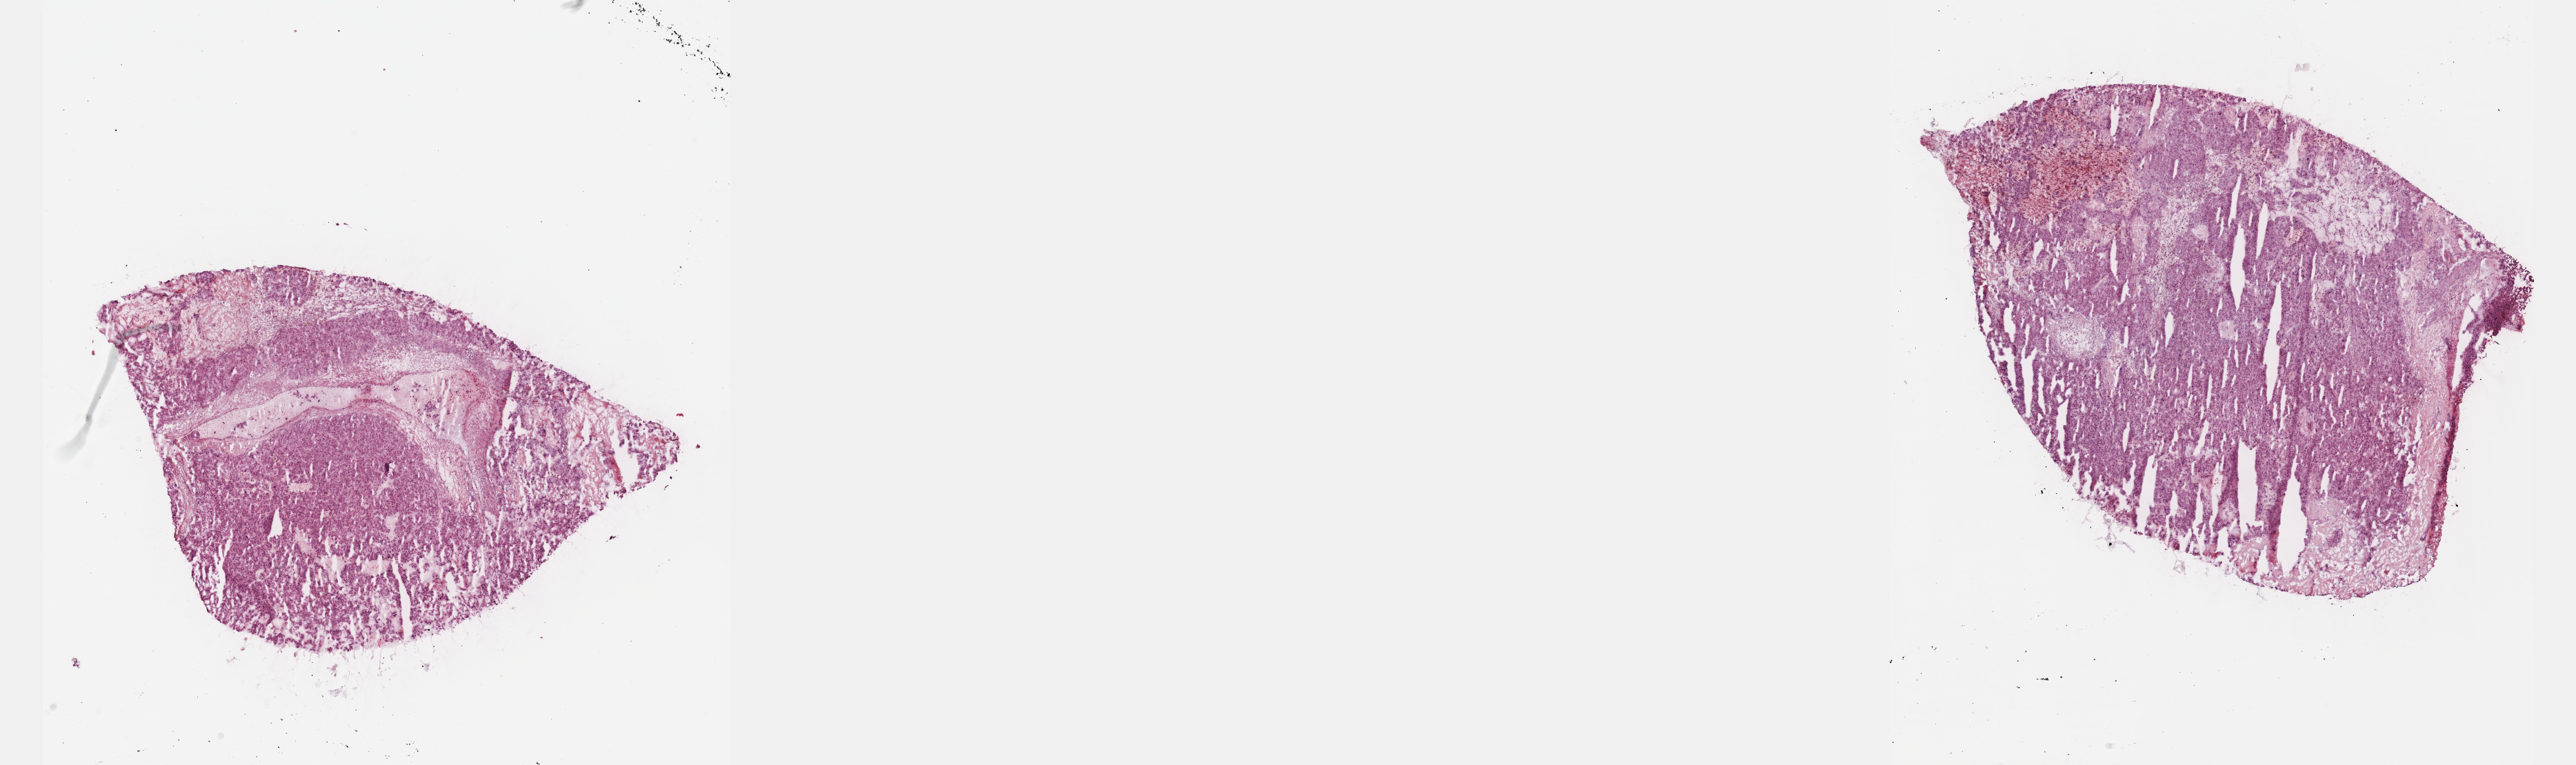
Digitized H&E tissue section (whole slide) — whole scanned area (about 30.2 x 9.0 mm, from a 40x scan) shown as a low-resolution overview, frozen section, sample: primary tumour, adrenal gland. Male patient; age at initial diagnosis 40 years.
Pathologic diagnosis: Pheochromocytoma, malignant.